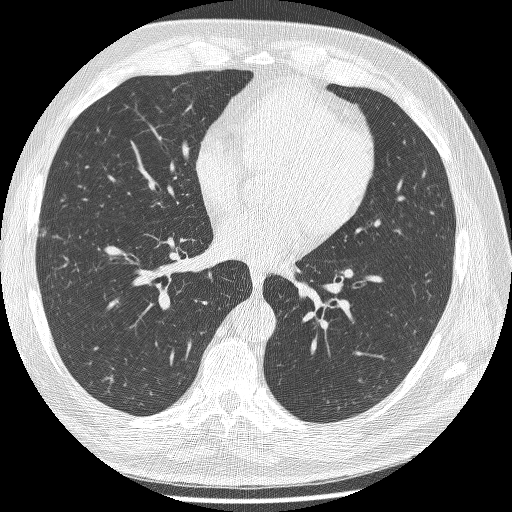
Low-dose screening chest CT, one axial slice. Slice 110 of 241 in the series (ordered by position). 120 kVp. Lung window (W 1500 / L -600 HU). 1.25 mm slice thickness. 512 × 512 image matrix, field of view 346 × 346 mm.
Structures marked on this image (manually delineated by an expert):
- lesion 1 (tumor, lower lobe of right lung): bounding box [x1, y1, x2, y2] px = [40, 229, 46, 237]